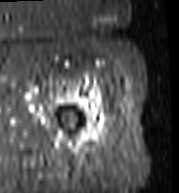
MRI of an extremity soft-tissue mass, one axial slice. Position 91 of 103 along the scan axis. STIR. MR volume resampled by the dataset authors to the PET/CT grid (not the native acquisition matrix). 3.27 mm slice thickness. 179 × 193 image matrix, field of view 175 × 188 mm. Female patient. Case-level facts recorded for this patient, not image findings: histological type: undifferentiated – high grade; grade: high; site of the primary tumour: left thigh.
Structures marked on this image (expert contour drawn on MRI and transferred to this co-registered scan by the dataset authors):
- gross tumour volume including surrounding oedema: bounding box (x1, y1, x2, y2) in pixels: (70, 87, 110, 156)
- gross tumour volume (mass): (79, 124, 106, 148)